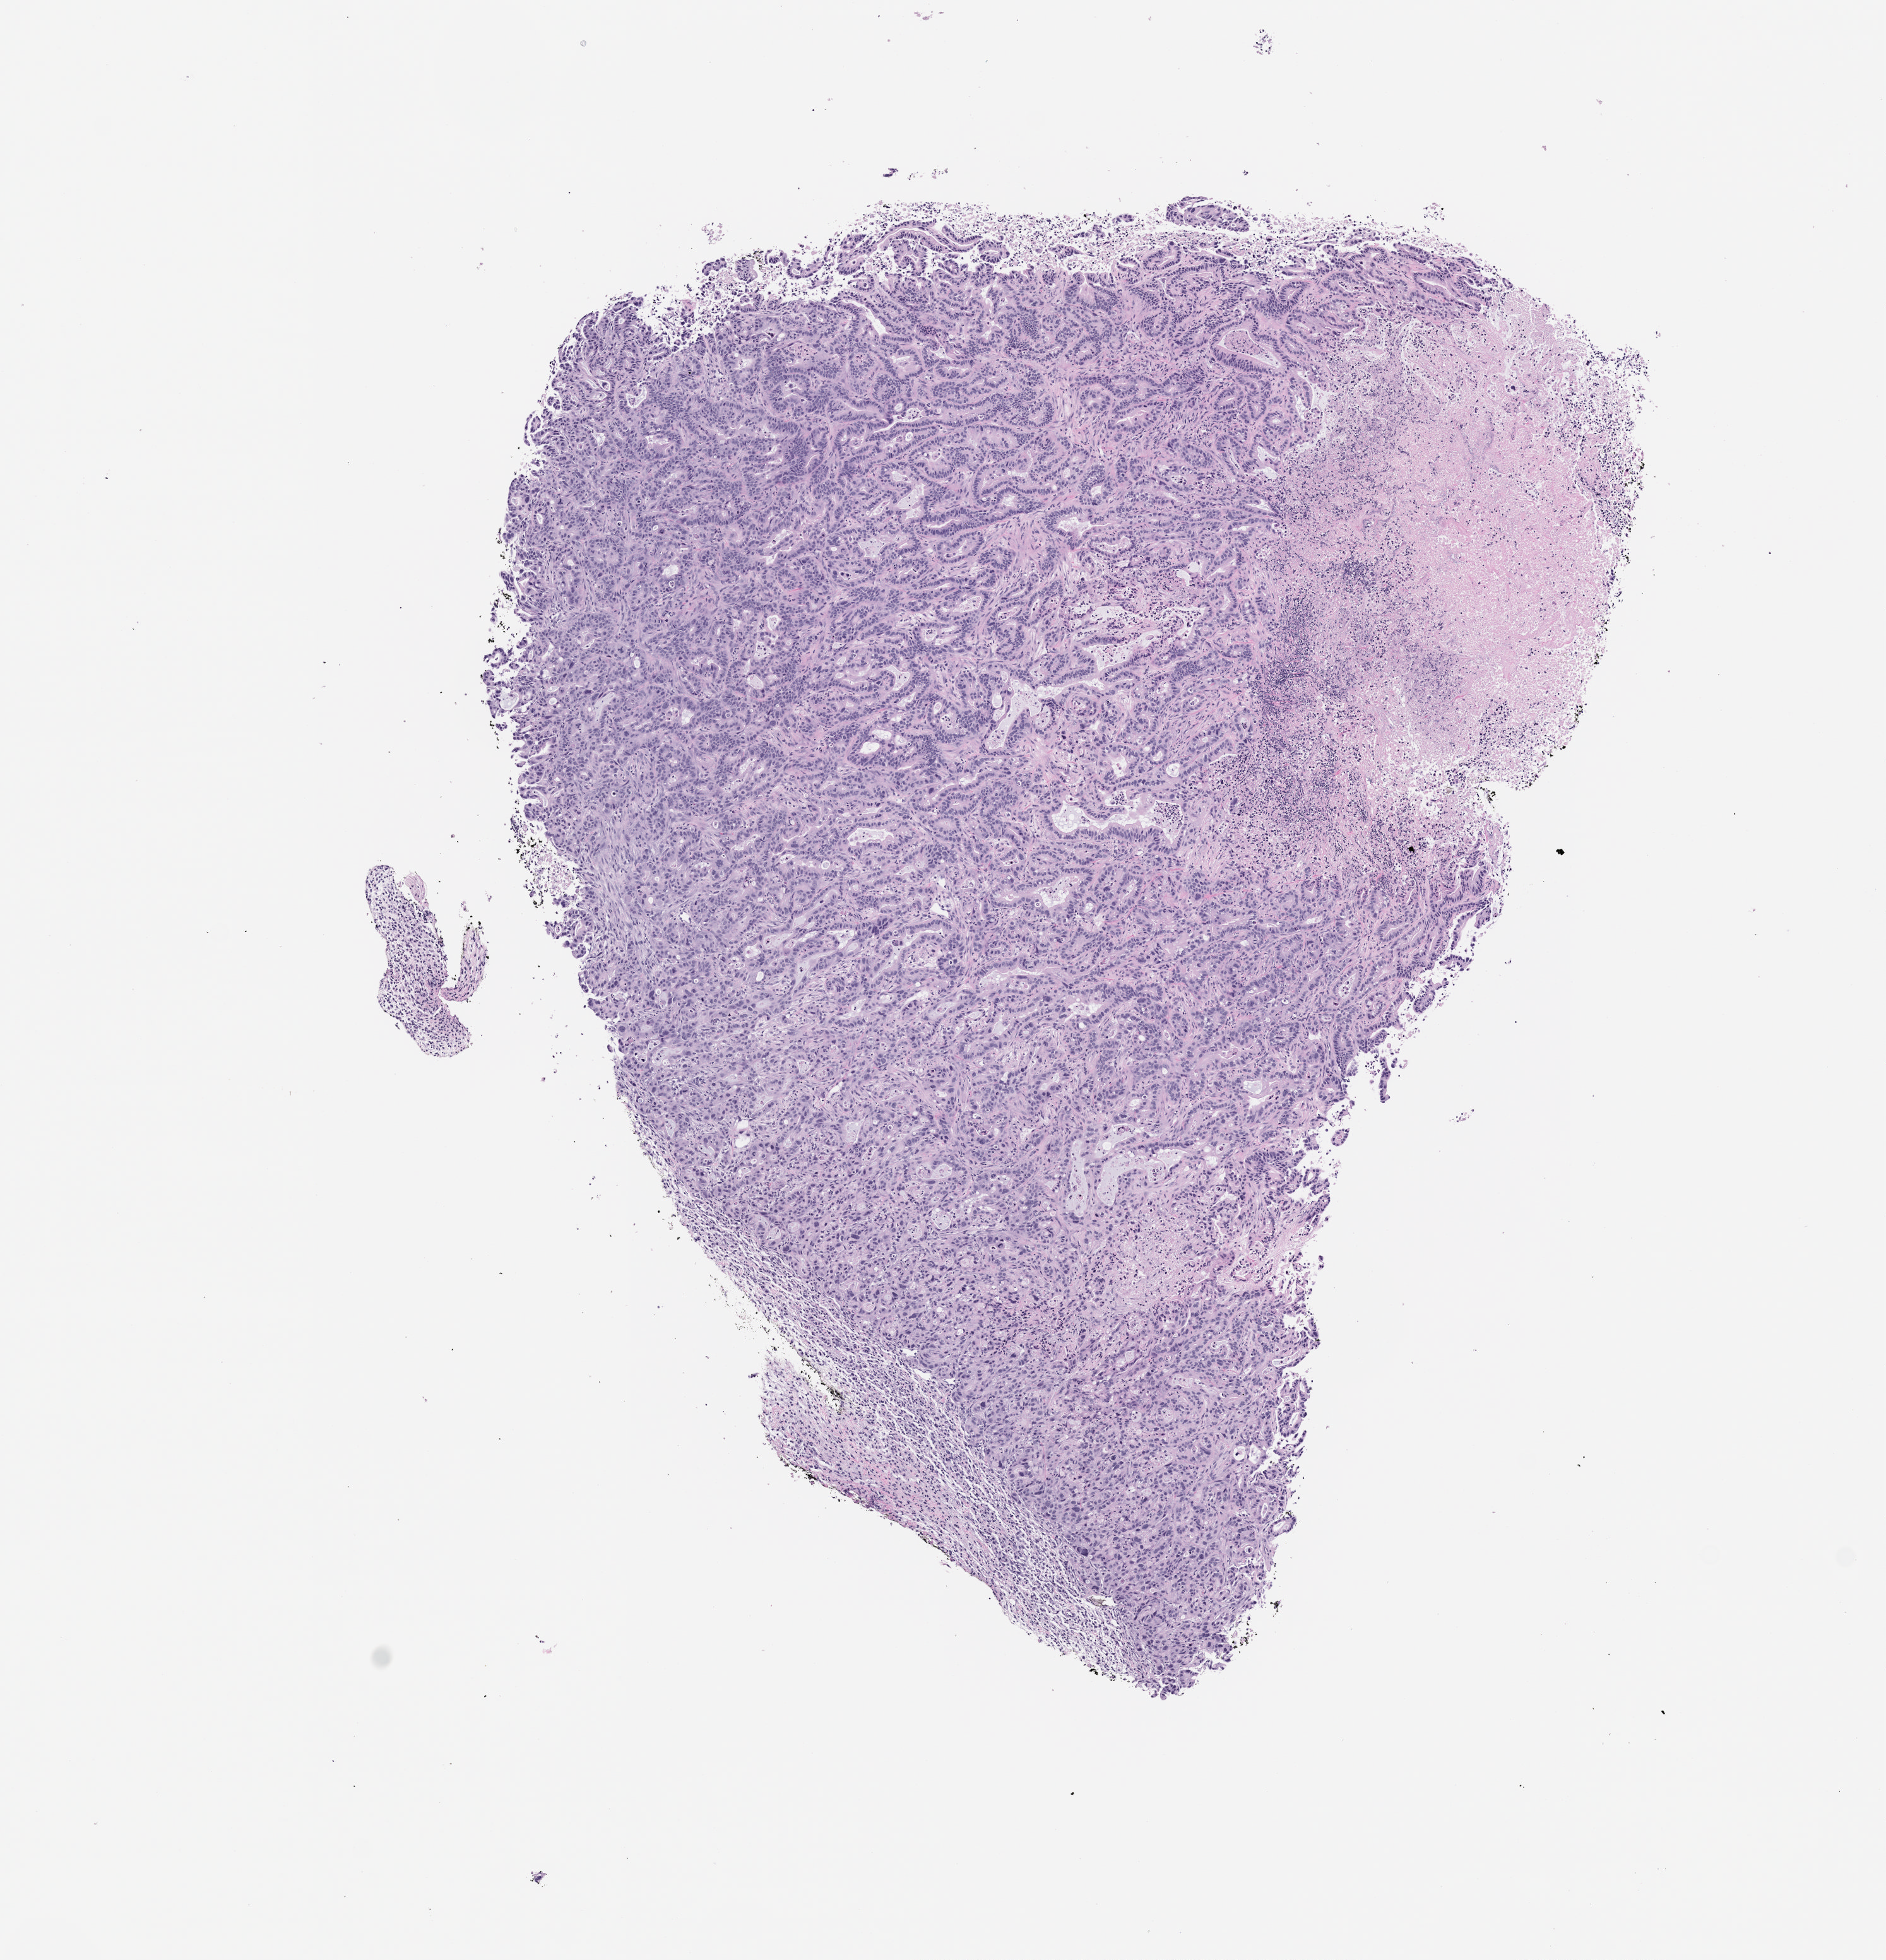
Haematoxylin and eosin whole-slide image of a patient-derived xenograft (PDX) tumor grown in a mouse, passage 1 — low-resolution overview of the scanned area, about 6.0 x 6.2 mm, formalin-fixed paraffin-embedded section, tumor site category: pancreas.
- originating patient diagnosis: Pancreatic Adenocarcinoma